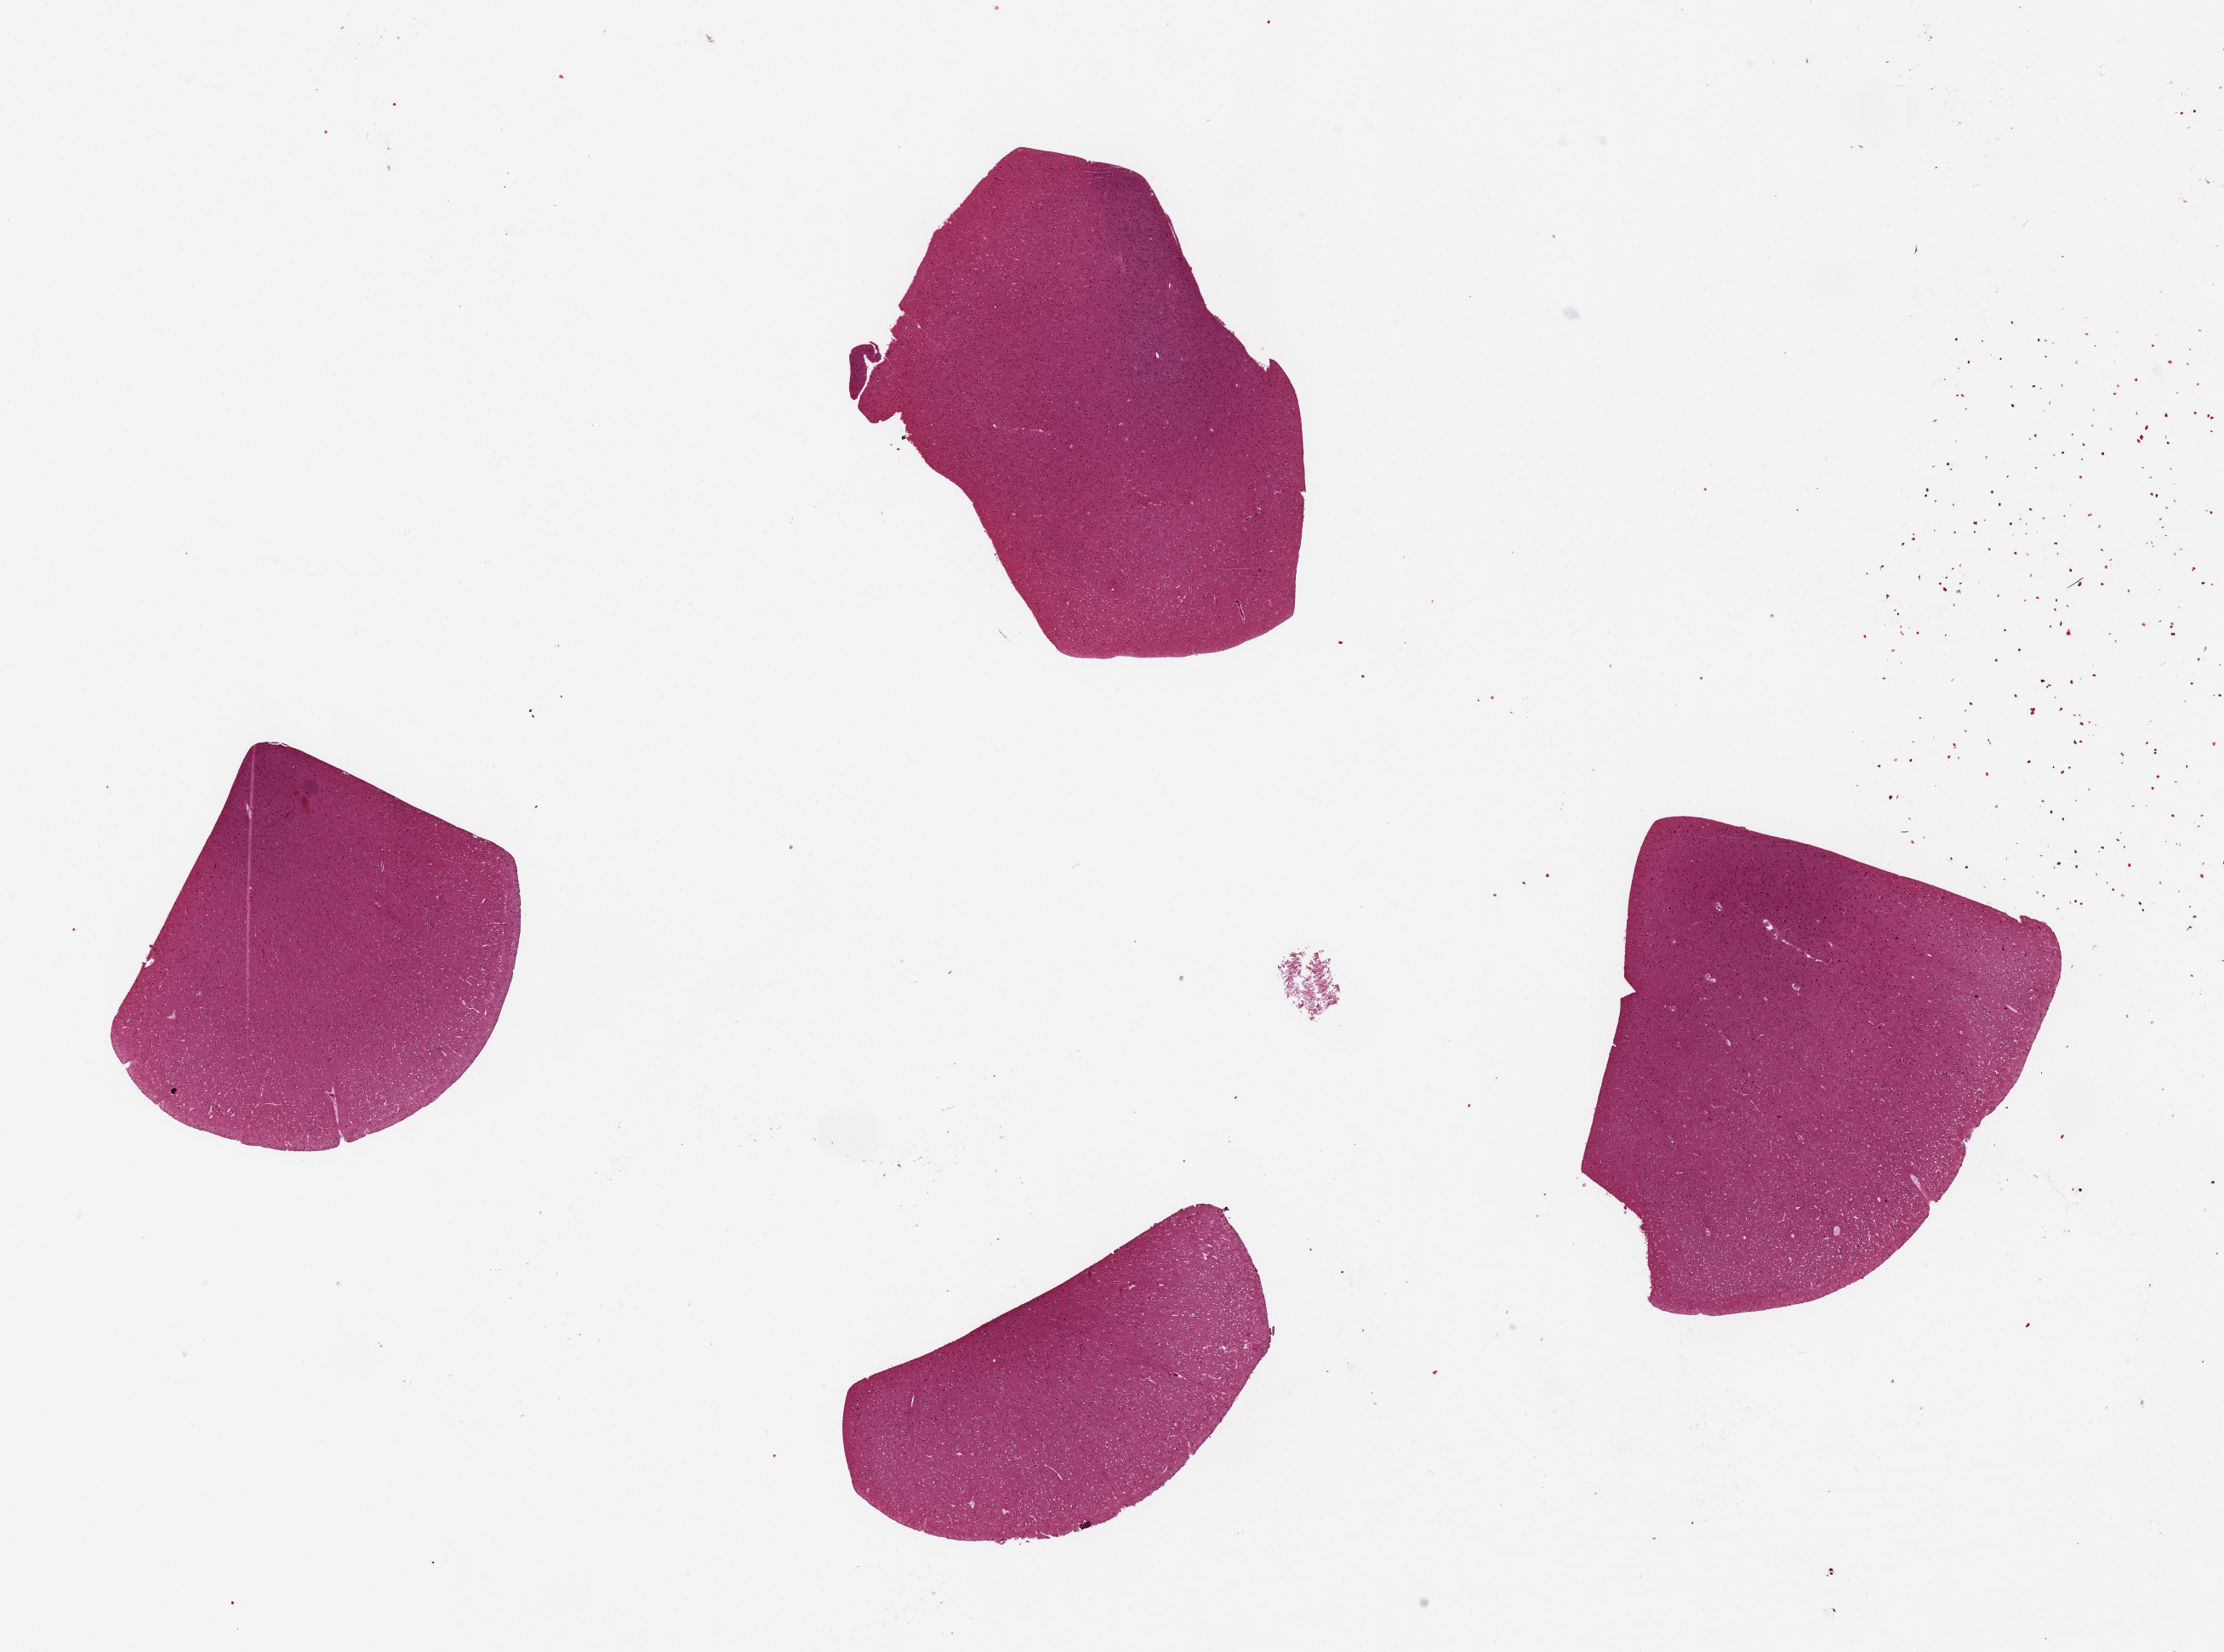
Haematoxylin and eosin whole-slide image — low-resolution overview of the scanned area, about 20.7 x 15.4 mm (from a 20x scan); PAXgene-fixed, paraffin-embedded tissue; target tissue: cerebral cortex; donor tissue sample.
Reviewer comment on this tissue sample: 4 pieces up to 4x4 mm.